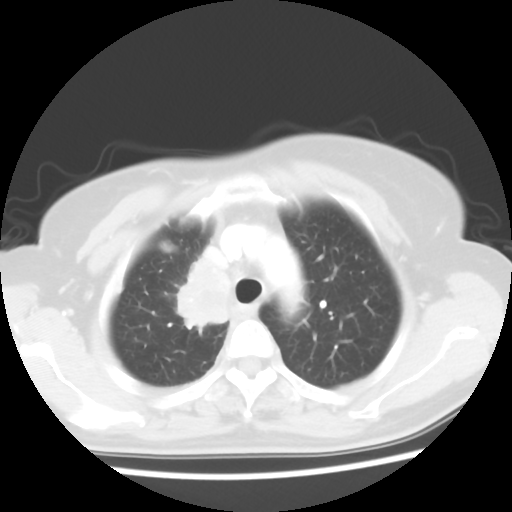
Chest CT, one axial slice. Slice 45 of 56 in the series (ordered by position). Lung window (W 1500 / L -600 HU). 512 × 512 image matrix, field of view 314 × 314 mm. Patient: female, 62 years. From the clinical record (not read from this slice): clinical TNM (as recorded): T2 N1 M1a.
Annotated regions visible in this slice (bounding box drawn by a radiologist):
- lung tumour (recorded histology: adenocarcinoma): bounding box (x1, y1, x2, y2) in pixels: (172, 249, 234, 336)